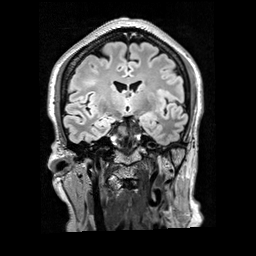
Brain MRI from a brain-tumour surgery series, one coronal slice; position 105 of 200 along the scan axis; T2 FLAIR; 256 × 256 image matrix. From the clinical record (not read from this slice): histopathology: Glioblastoma; WHO grade: 4; IDH mutation: no.
Outlined on this slice (outlined manually by an expert reader):
- tumour: bounding box (x1, y1, x2, y2) in pixels: (85, 72, 98, 86)